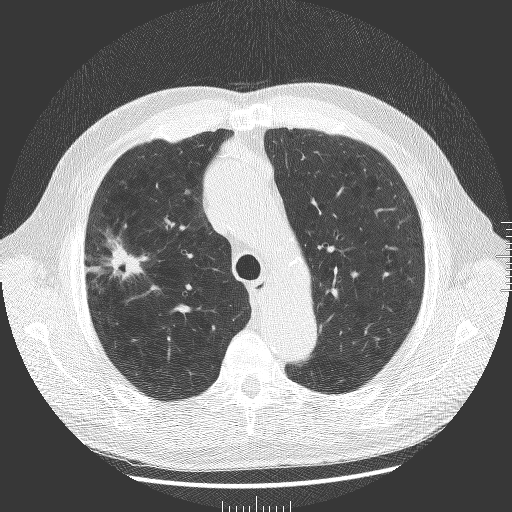
Low-dose screening chest CT, one axial slice; slice 137 of 181 in the series (ordered by position); reconstruction kernel BONE; lung window (W 1500 / L -600 HU); 2 mm slice thickness; 512 × 512 image matrix, field of view 380 × 380 mm.
Outlined on this slice (expert manual segmentation):
- lesion 1 (tumor, upper lobe of right lung): bounding box (x1, y1, x2, y2) in pixels: (108, 238, 142, 279)